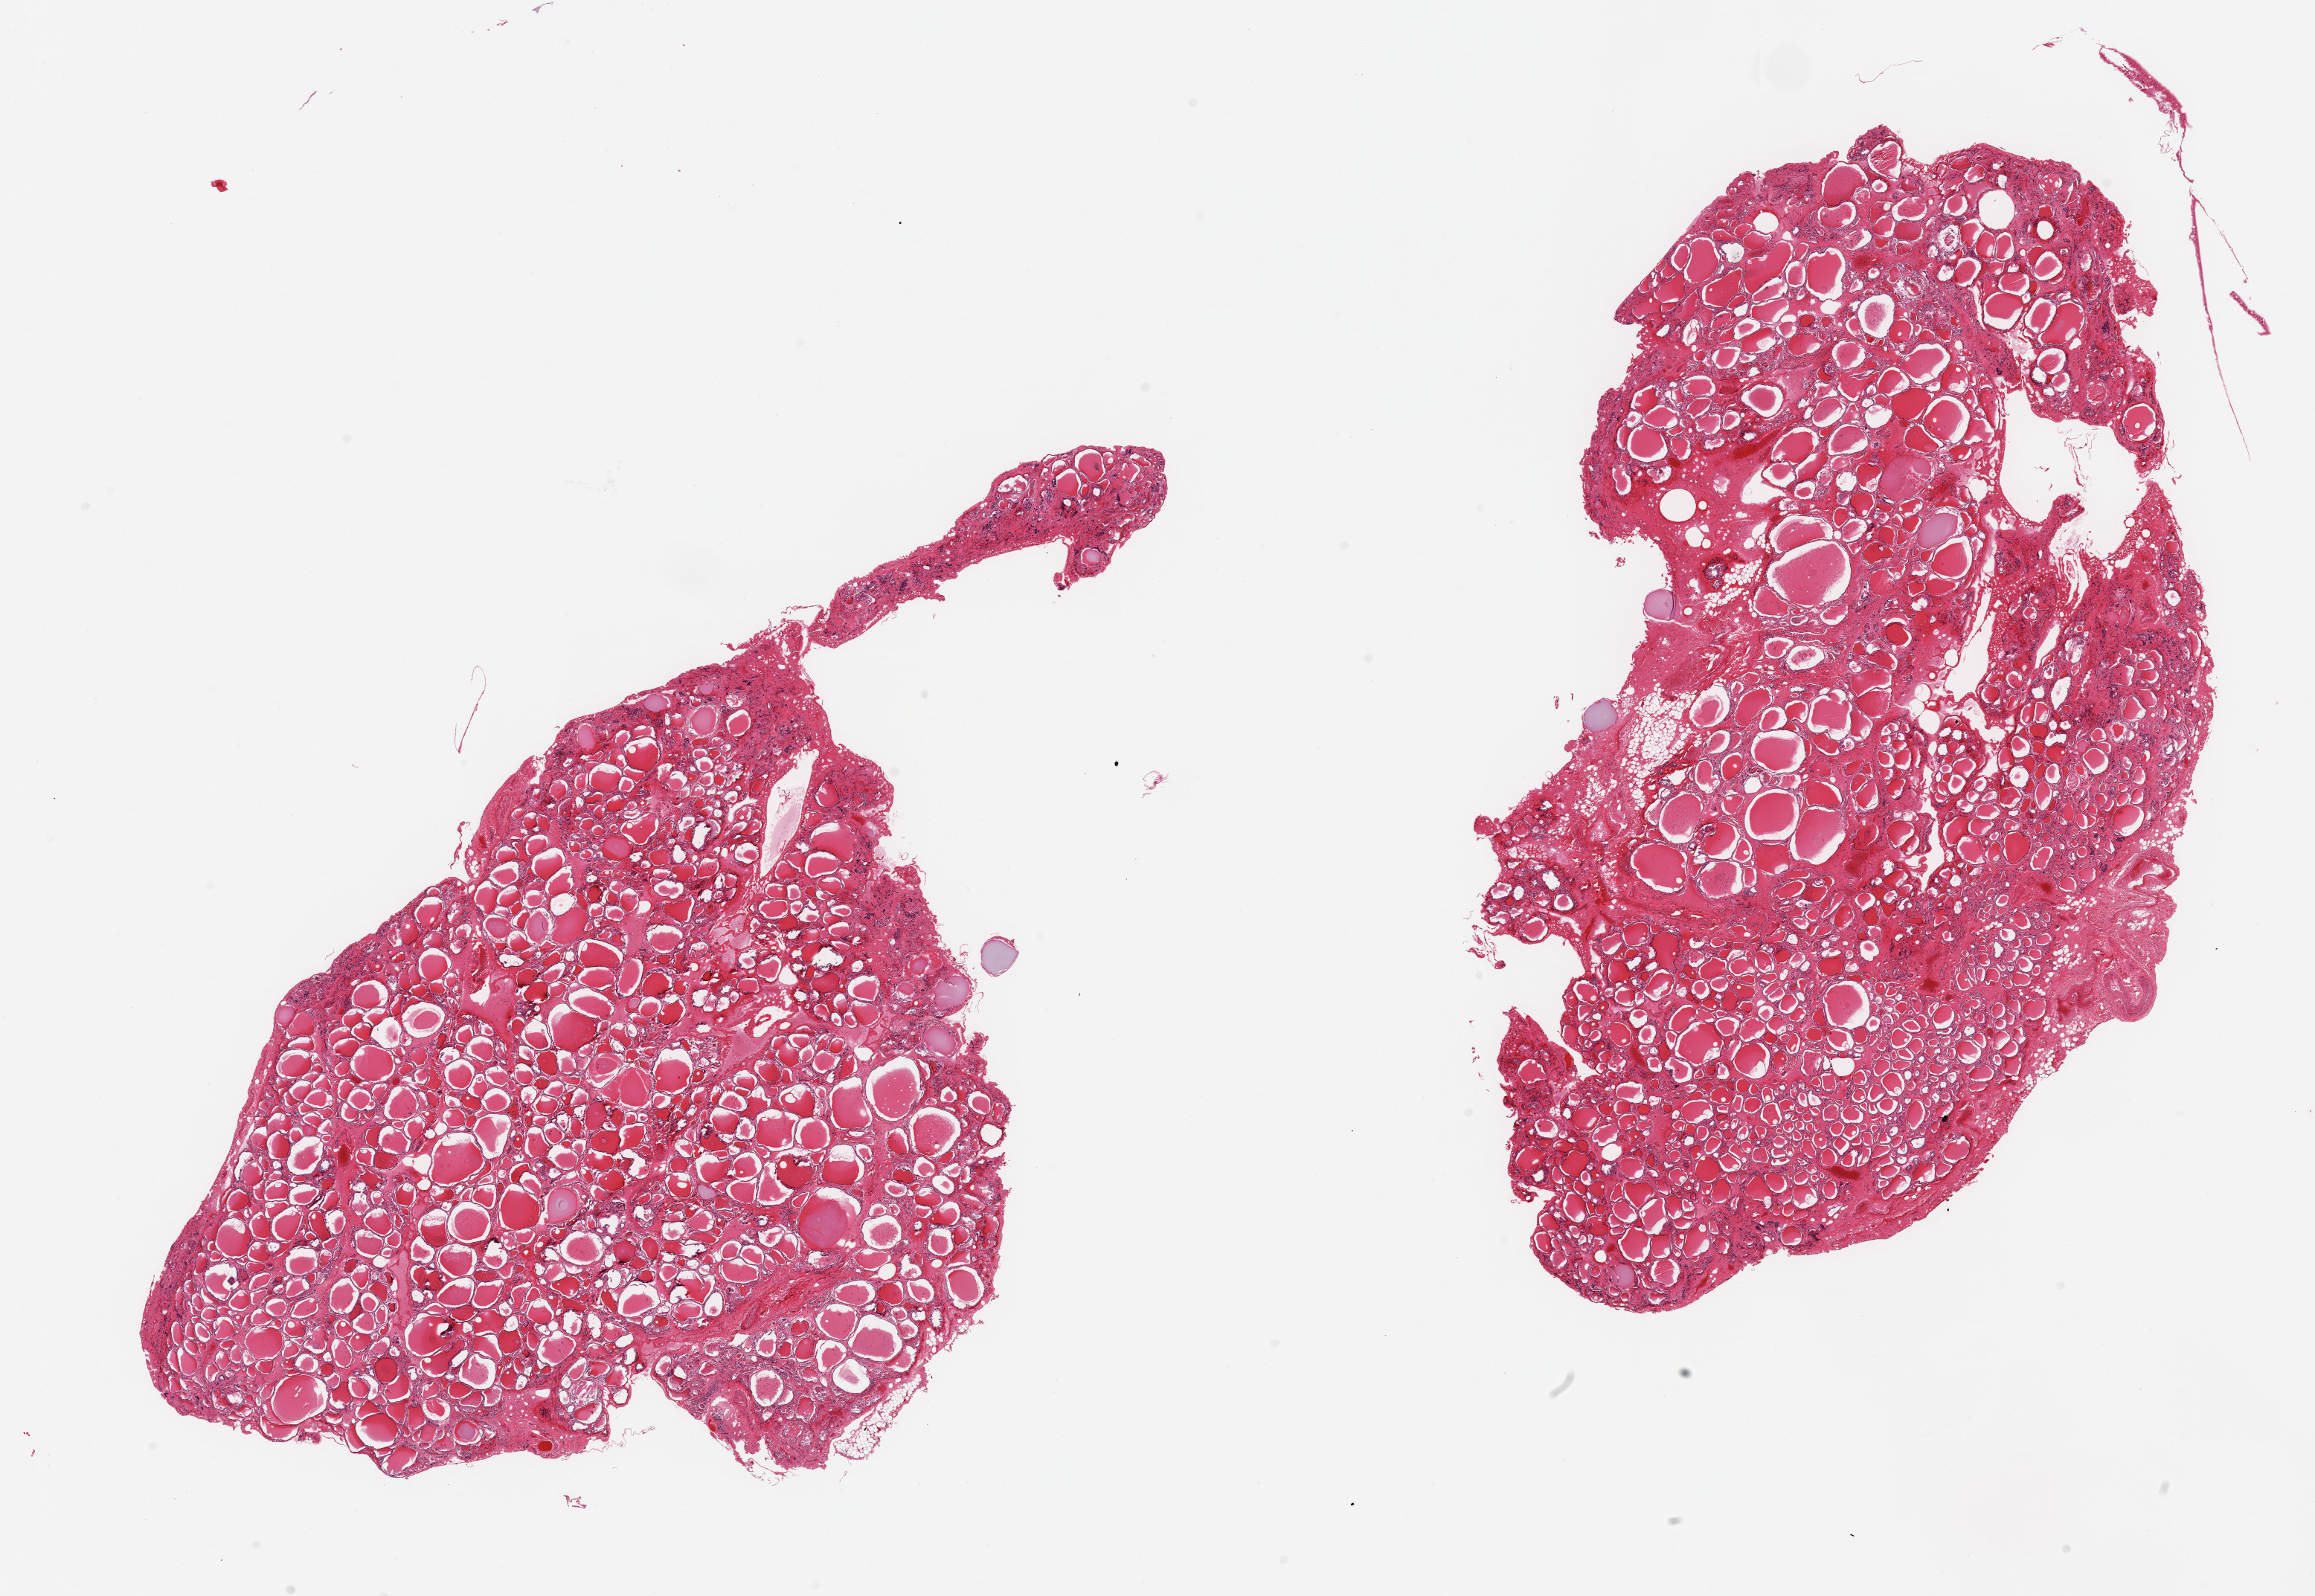
Whole-slide image, haematoxylin and eosin stain, whole scanned area (about 24.6 x 17.0 mm) shown as a low-resolution overview, PAXgene-fixed paraffin-embedded (PFPE) section, section of thyroid (target tissue), tissue donor sample. Donor: male.
Review note (as recorded): 2 pieces; mild interstitial fibrosis and trivial external fat.